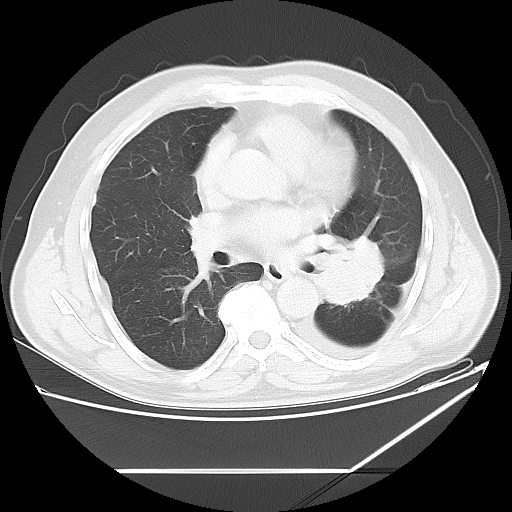
Chest CT, one axial slice; slice 31 of 60 in the series (ordered by position); reconstruction kernel LUNG; lung window (W 1500 / L -600 HU); 5 mm slice thickness; 512 × 512 image matrix, field of view 395 × 395 mm. Patient: male, 62 years. Case-level facts recorded for this patient, not image findings: clinical TNM (as recorded): T3 N0 M1.
Structures marked on this image (bounding box drawn by a radiologist):
- lung tumour (recorded histology: adenocarcinoma): bounding box [x1, y1, x2, y2] px = [320, 227, 390, 311]
- lung tumour (recorded histology: adenocarcinoma): [323, 225, 392, 311]